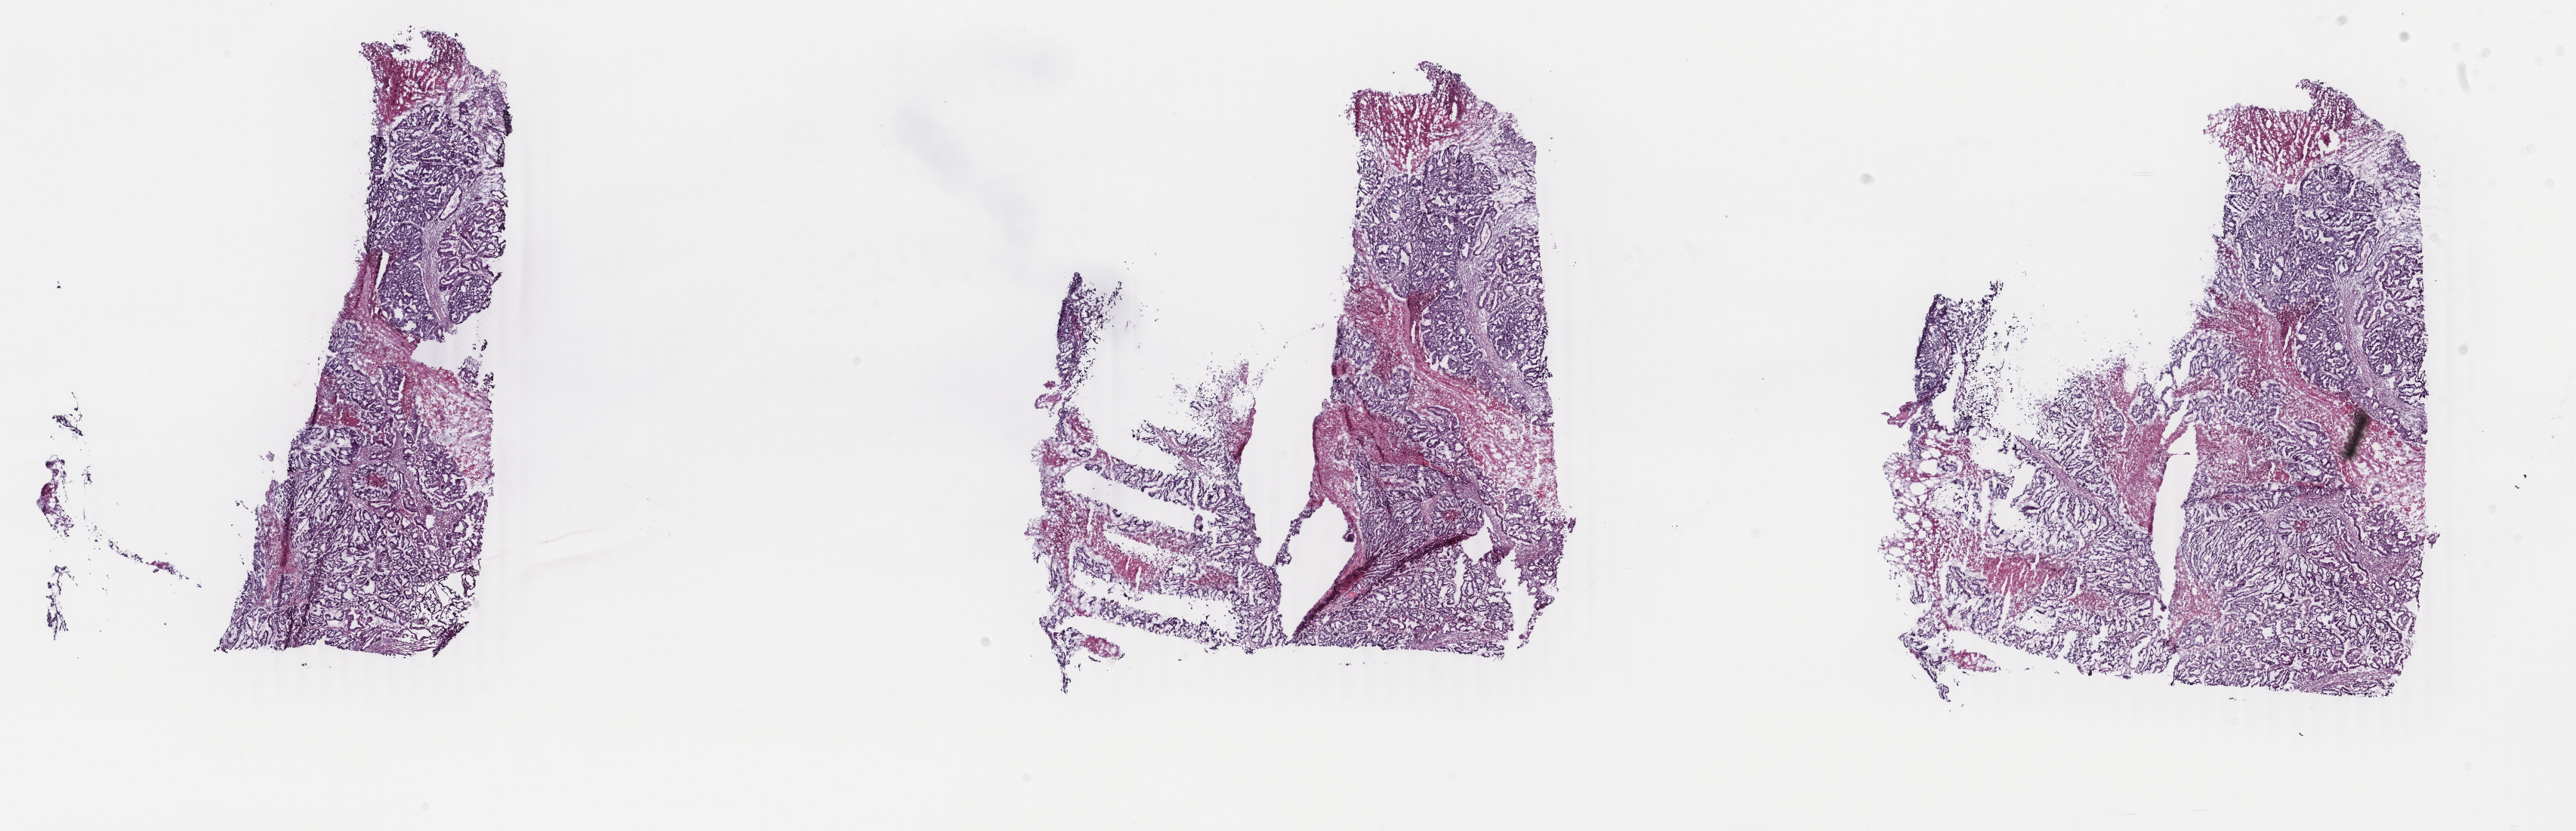
Digitized H&E-stained tissue section (whole slide) — low-resolution overview of the scanned area, about 27.1 x 8.7 mm, frozen section, primary tumour sample from the uterus. Female patient; age at initial diagnosis 70 years. Histologic grade: G2 (moderately differentiated). Slide review estimates, as recorded: tumour cells 60%, tumour nuclei 60%, normal cells 0%, stromal cells 30%, necrosis 10%. Inflammatory infiltration, as recorded: lymphocyte infiltration 40%, monocyte infiltration 20%, neutrophil infiltration 20%.
• FIGO stage: IB
• diagnosis: Endometrioid adenocarcinoma, NOS (endometrium)